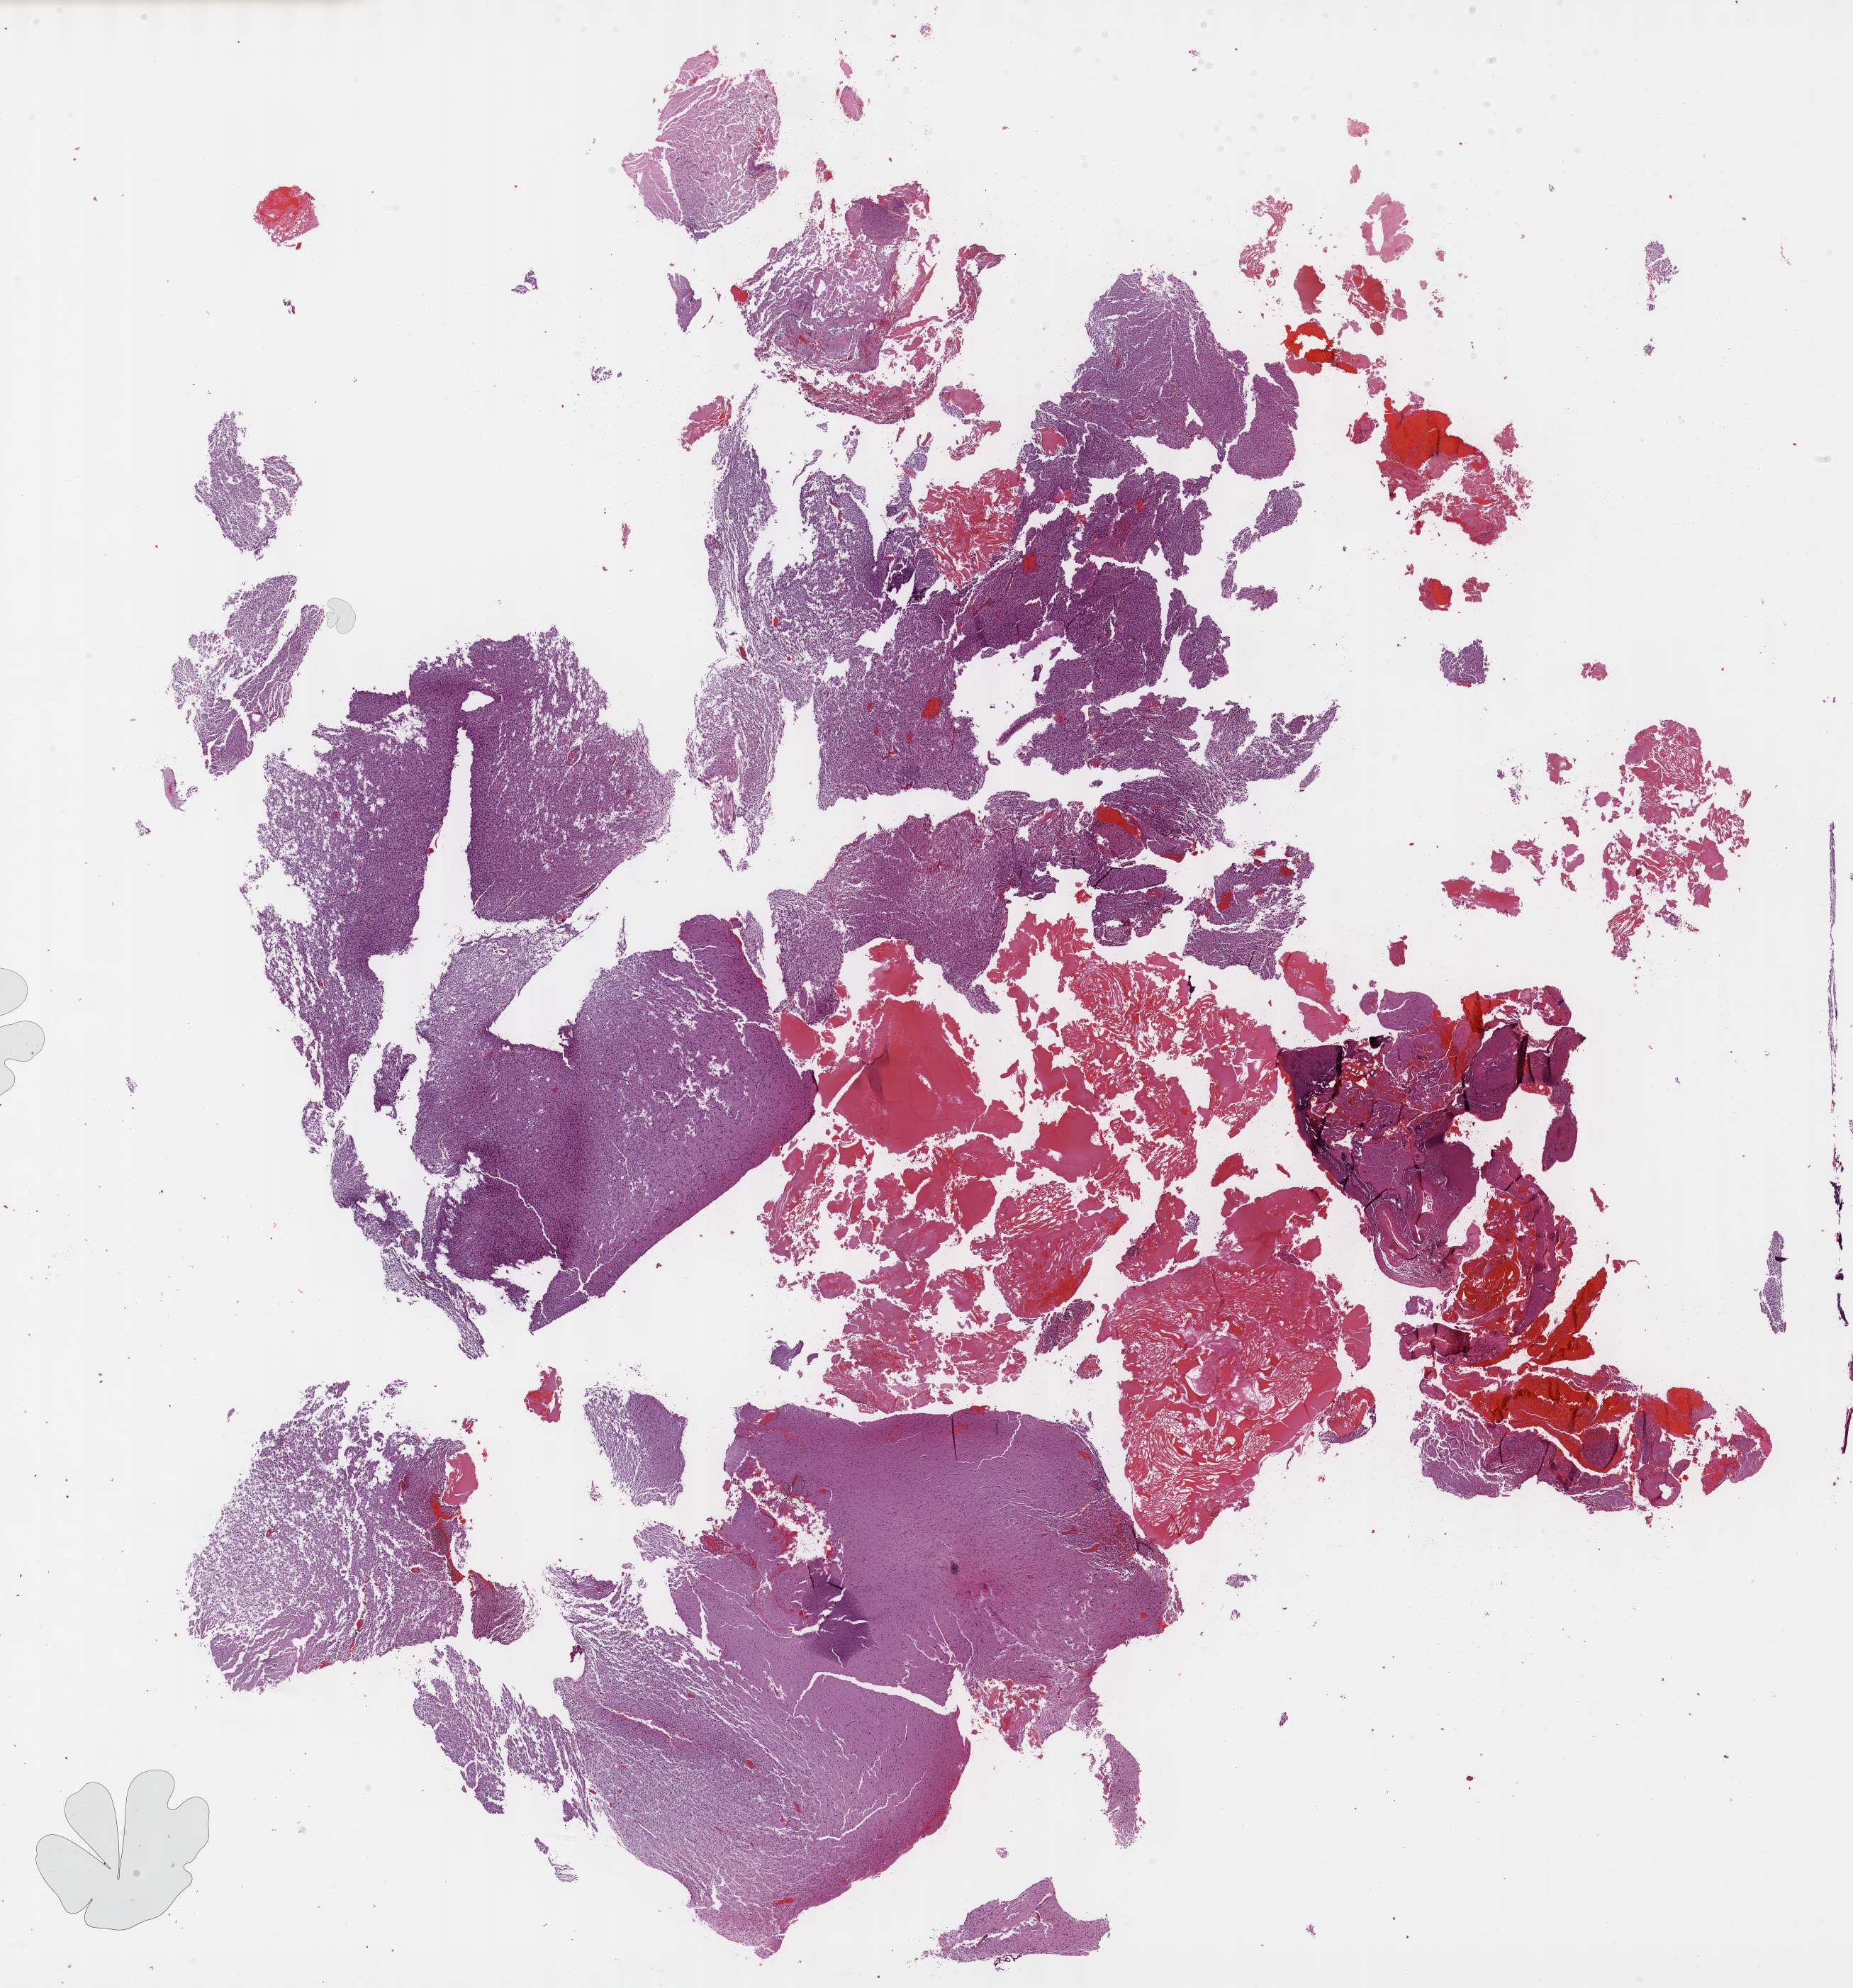
H&E whole-slide image — whole scanned area (about 21.1 x 22.7 mm, slide scanned at 40x) shown as a low-resolution overview. Formalin-fixed paraffin-embedded (FFPE) diagnostic section. Sample: primary tumour, brain. Male, age 34 years at initial diagnosis. Histologic grade: G3 (poorly differentiated).
Laterality: left. Diagnosis: Astrocytoma, anaplastic (cerebrum).